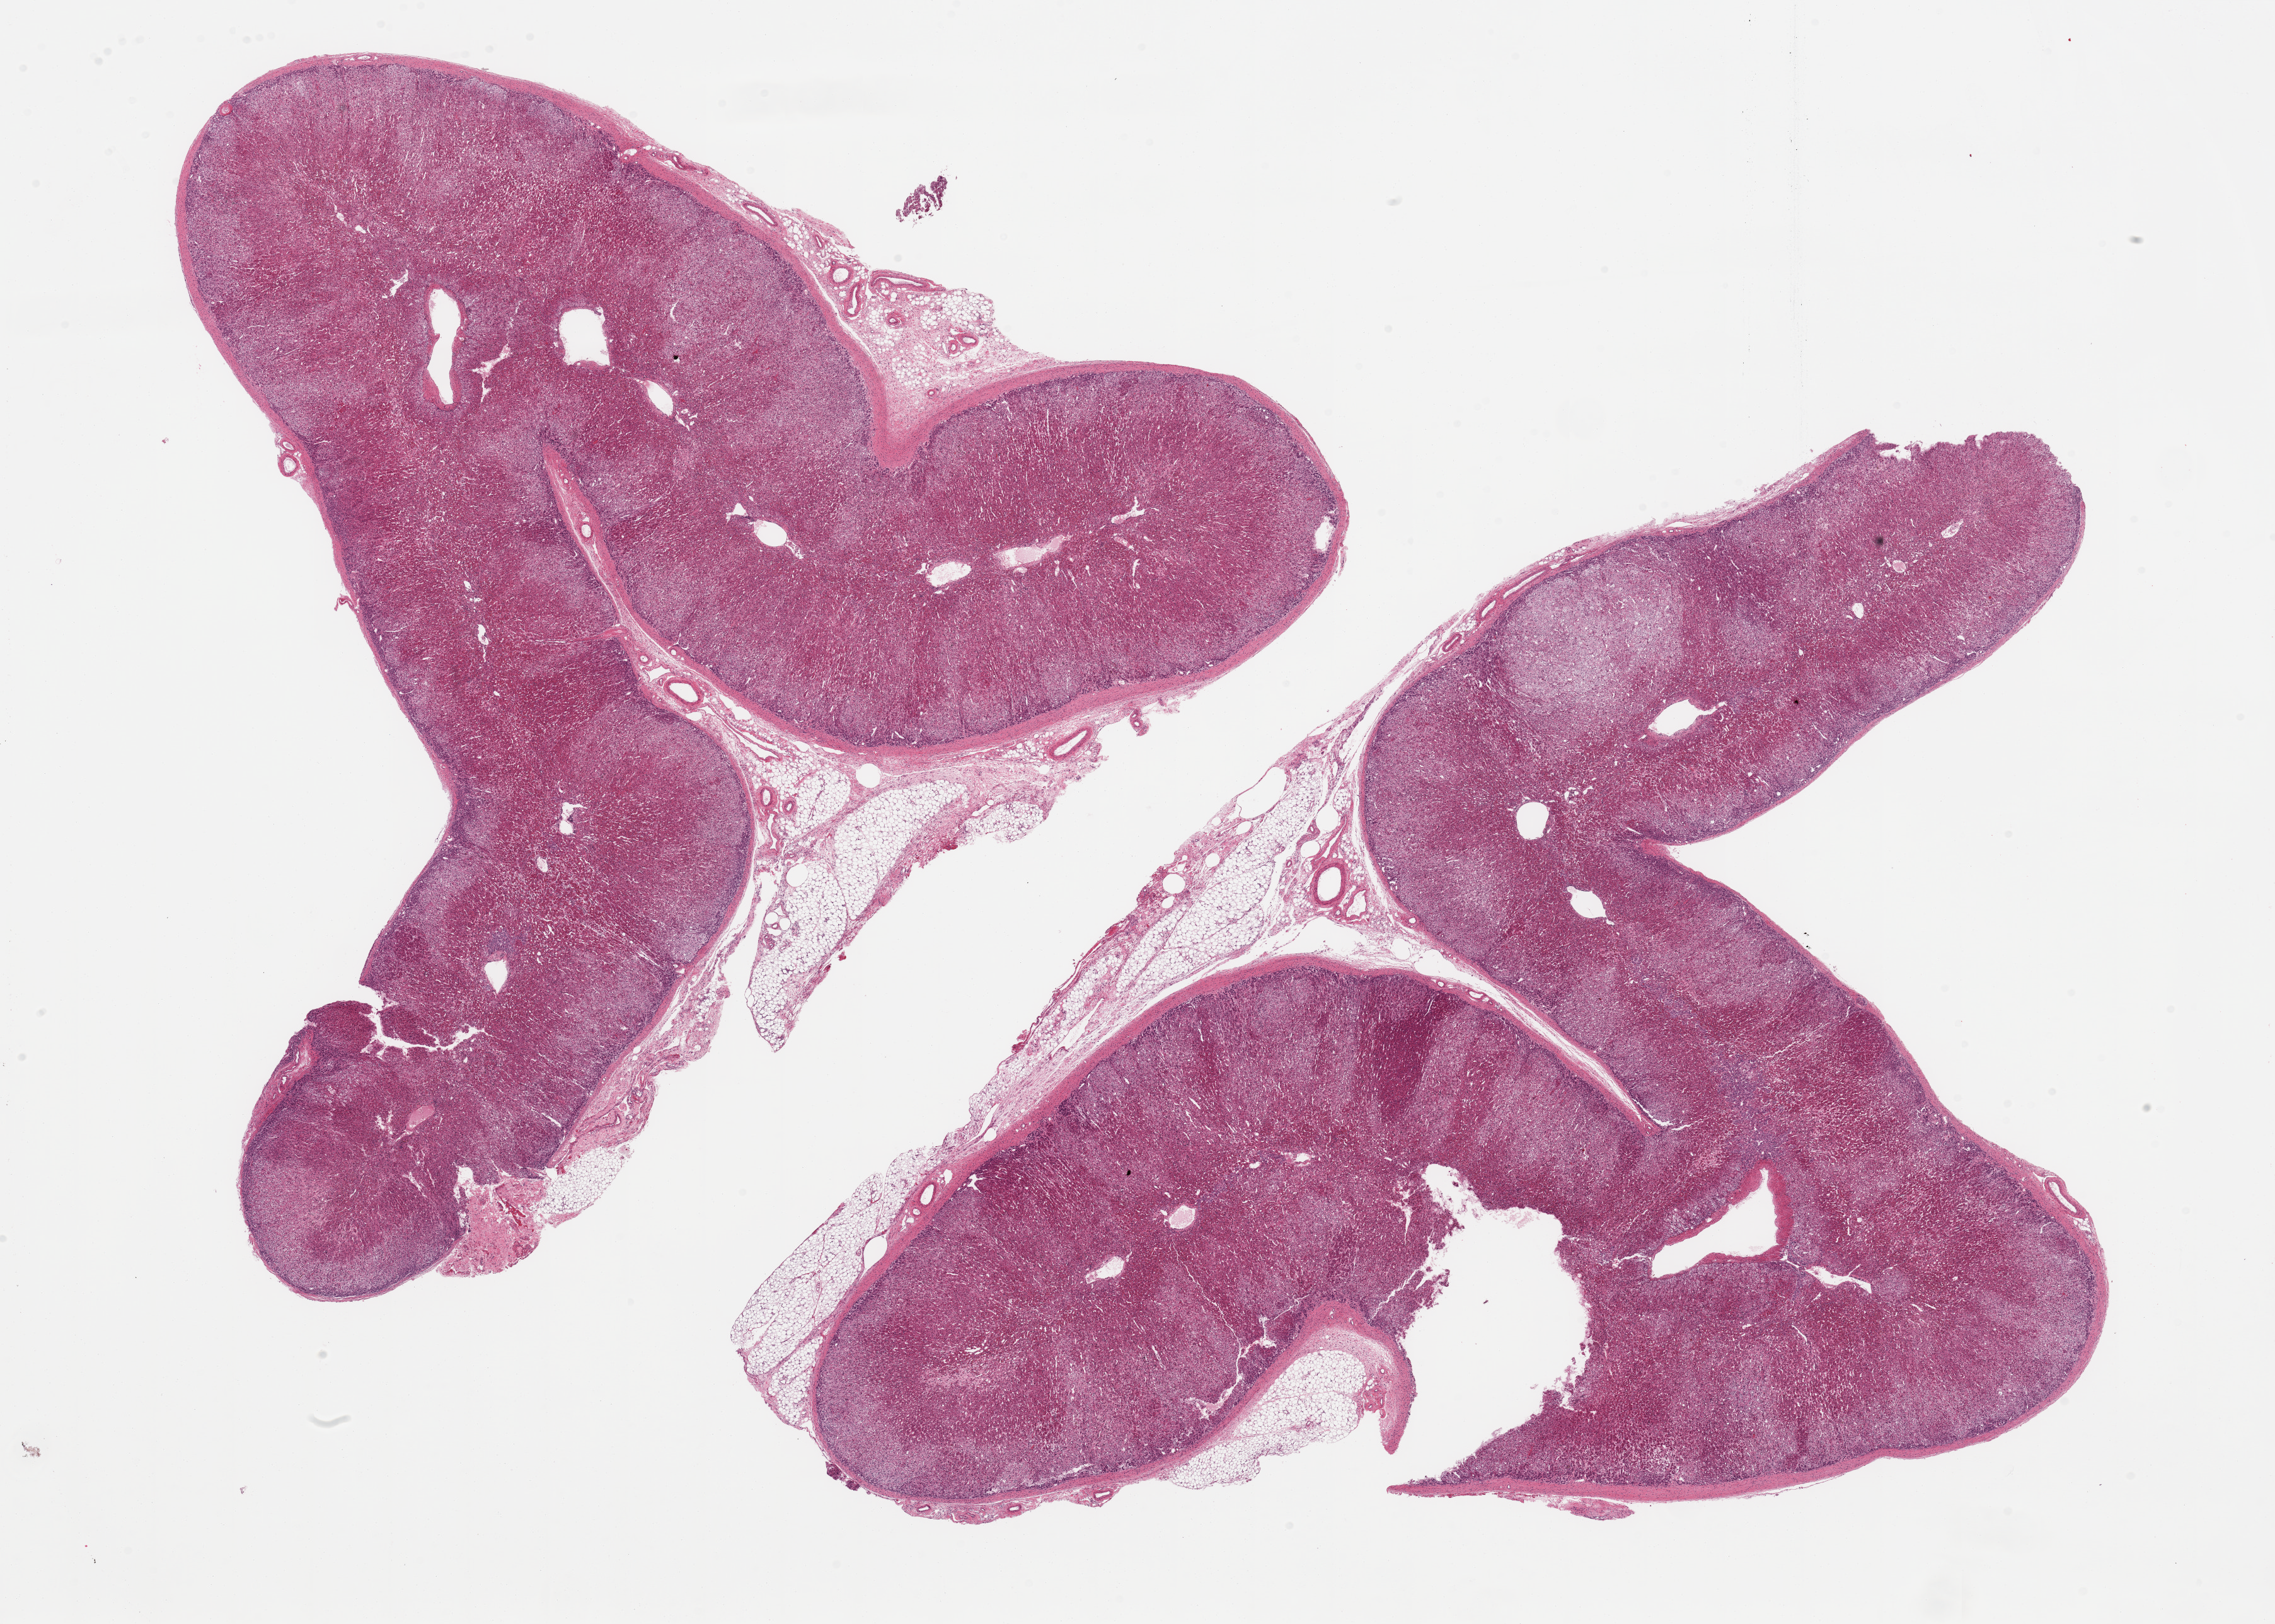
Digitized hematoxylin and eosin (H&E)-stained section, brightfield, whole scanned area (about 28.5 x 20.4 mm, acquisition: 20x scan) shown as a low-resolution overview; PAXgene-fixed, paraffin-embedded tissue; sampled site (target tissue): adrenal gland; tissue donor sample. Donor: male.
Reviewer comment on this tissue sample: 2 pieces, well preserved cortex, only trace adherent fat.